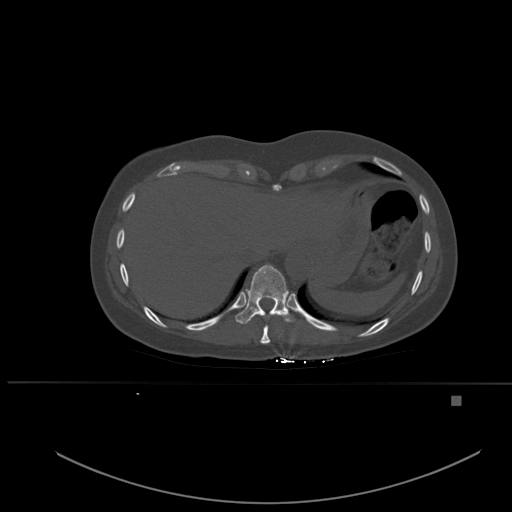
CT including the spine, one axial slice; slice 294 of 651 in the series (ordered by position); bone window (W 1800 / L 400 HU); 1.5 mm slice thickness; 512 × 512 image matrix, field of view 443 × 443 mm. Patient: female, 49 years. Case-level facts recorded for this patient, not image findings: primary cancer: breast; vertebrae with lytic lesions (as recorded): L3, T12, L4.
Annotated regions visible in this slice (semi-automatically segmented with operator editing):
- T10 vertebra: bounding box (x1, y1, x2, y2) in pixels: (235, 265, 295, 324)
- T9 vertebra: (253, 314, 272, 344)